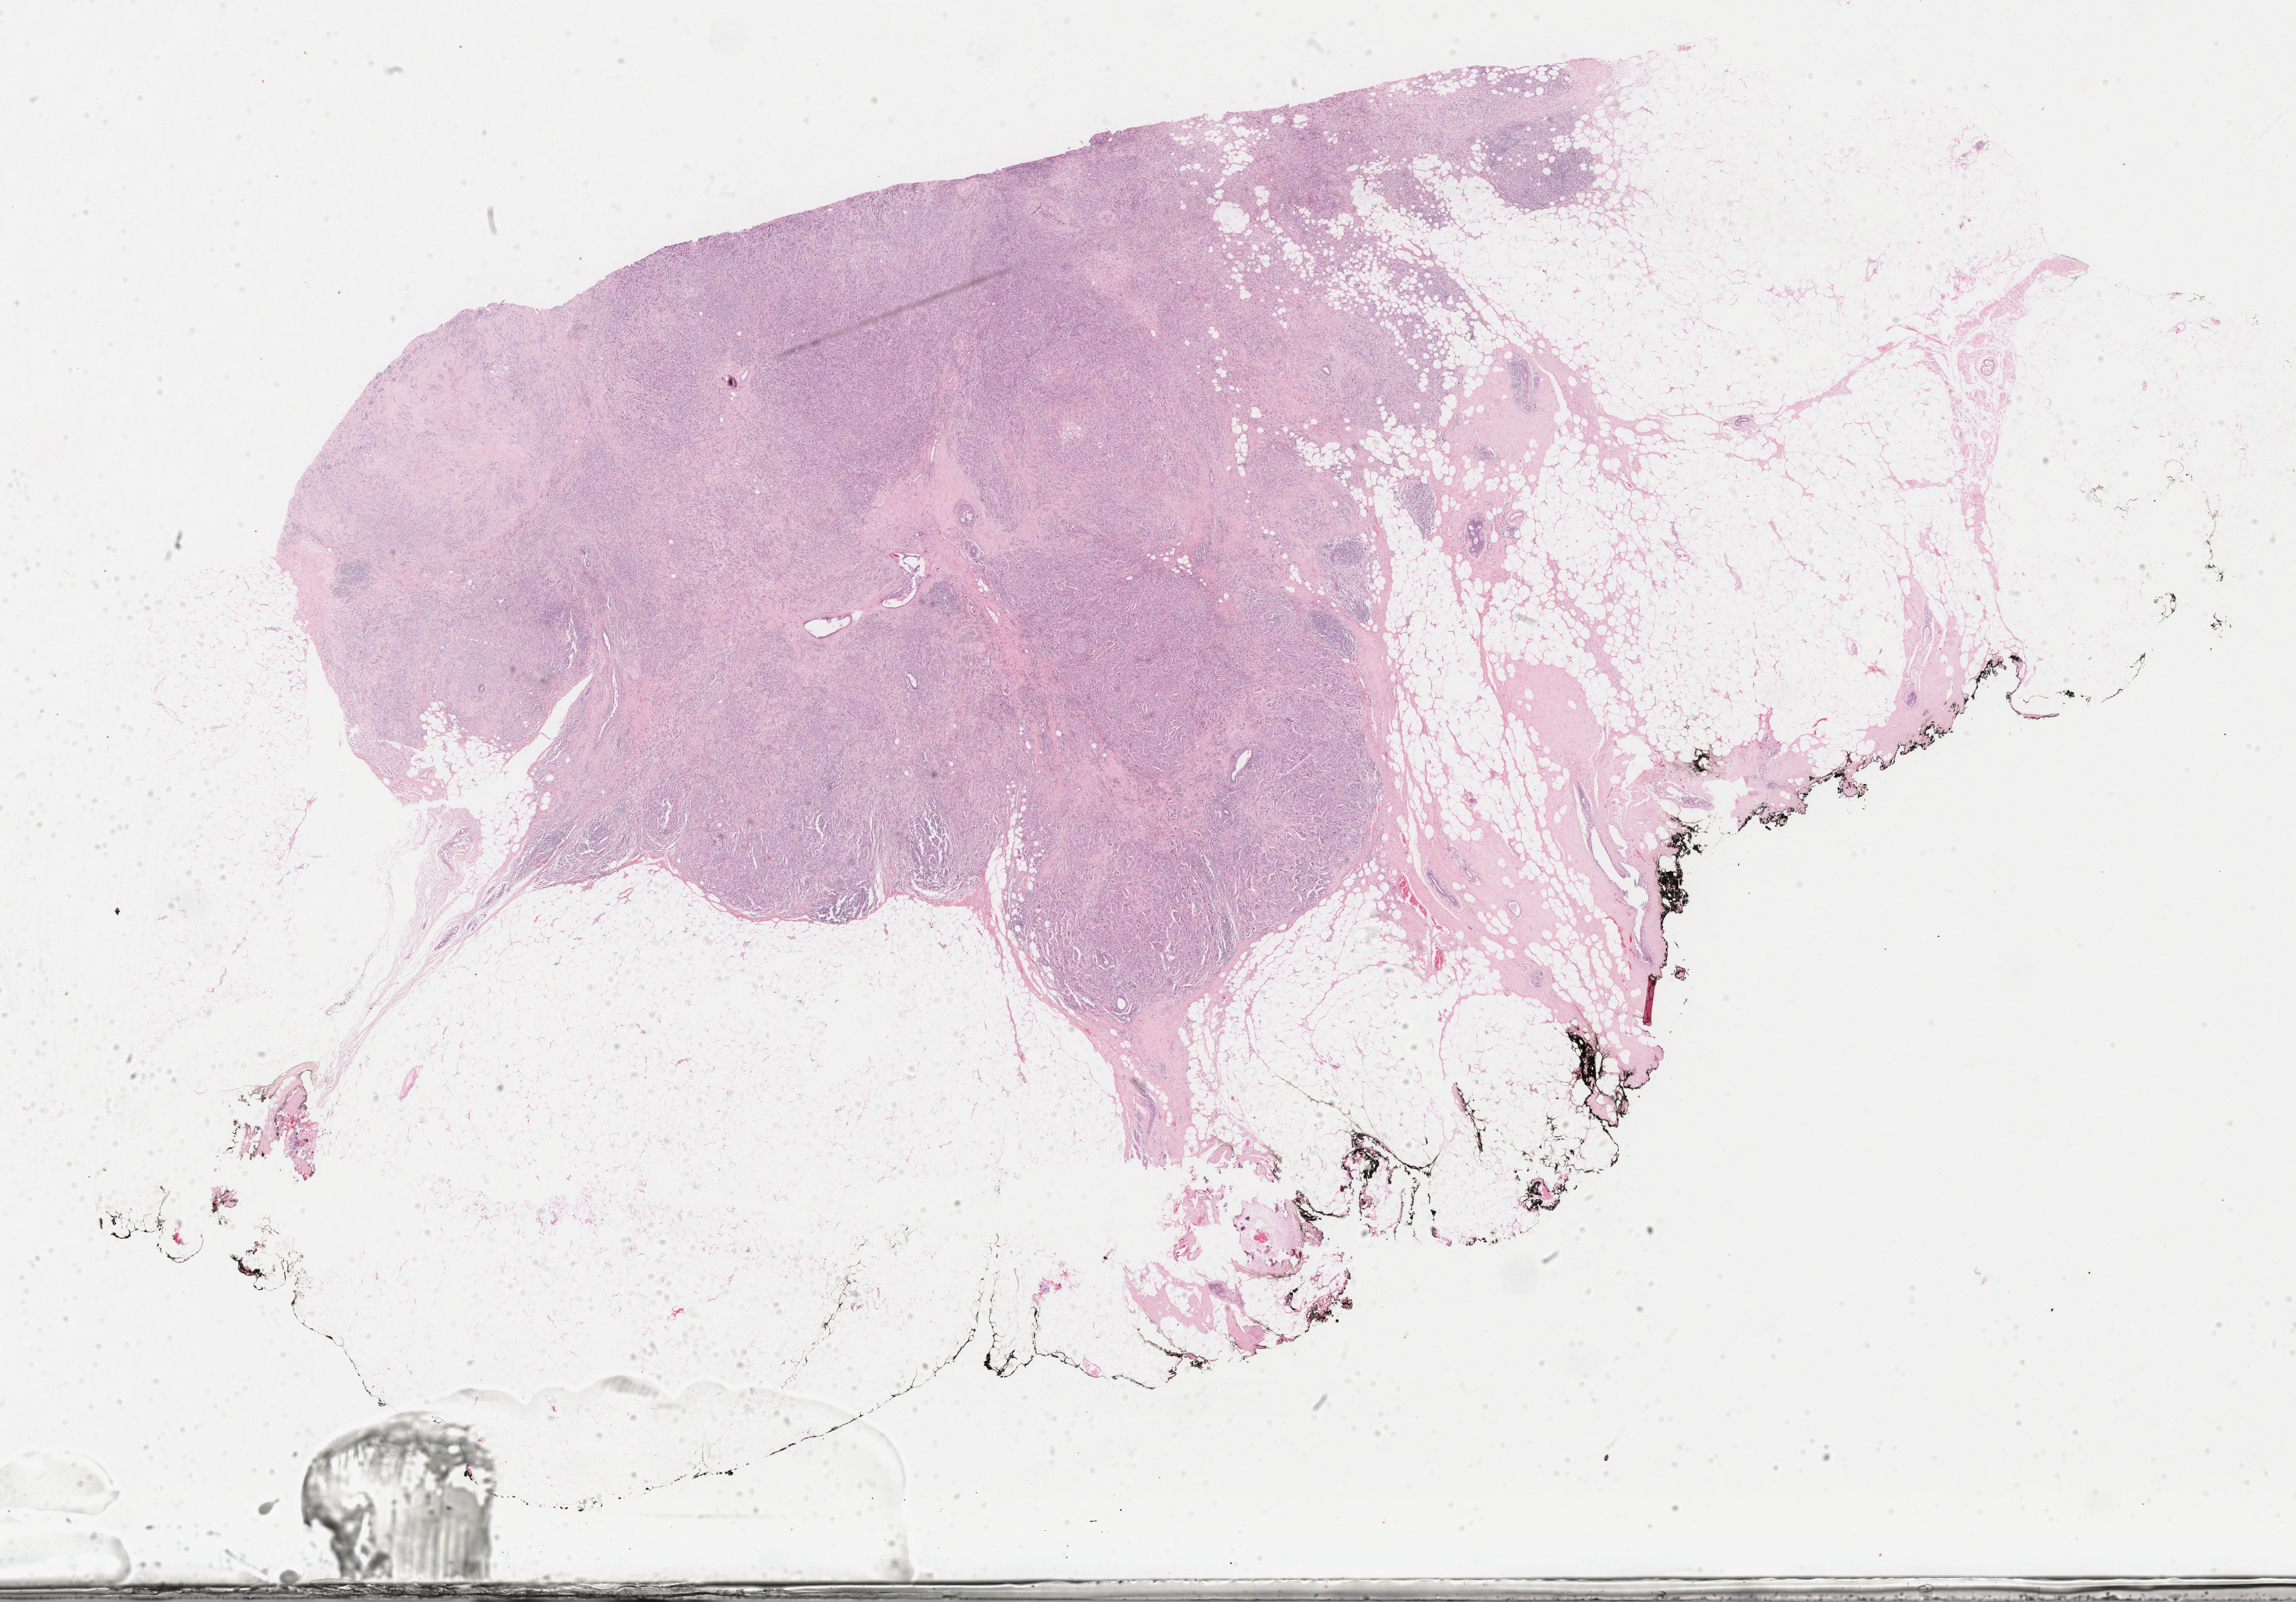
Digitized Hematoxylin and eosin (H&E) stained tissue section (whole slide), a low-resolution overview of the entire scanned area, about 30.2 x 21.1 mm (from a 40x scan). Formalin-fixed paraffin-embedded (FFPE) diagnostic section. Primary tumour sample from the breast. Patient: female, age at initial diagnosis 82 years.
AJCC pathologic stage: IV. Histologic diagnosis: Infiltrating duct carcinoma, NOS. Laterality: right.